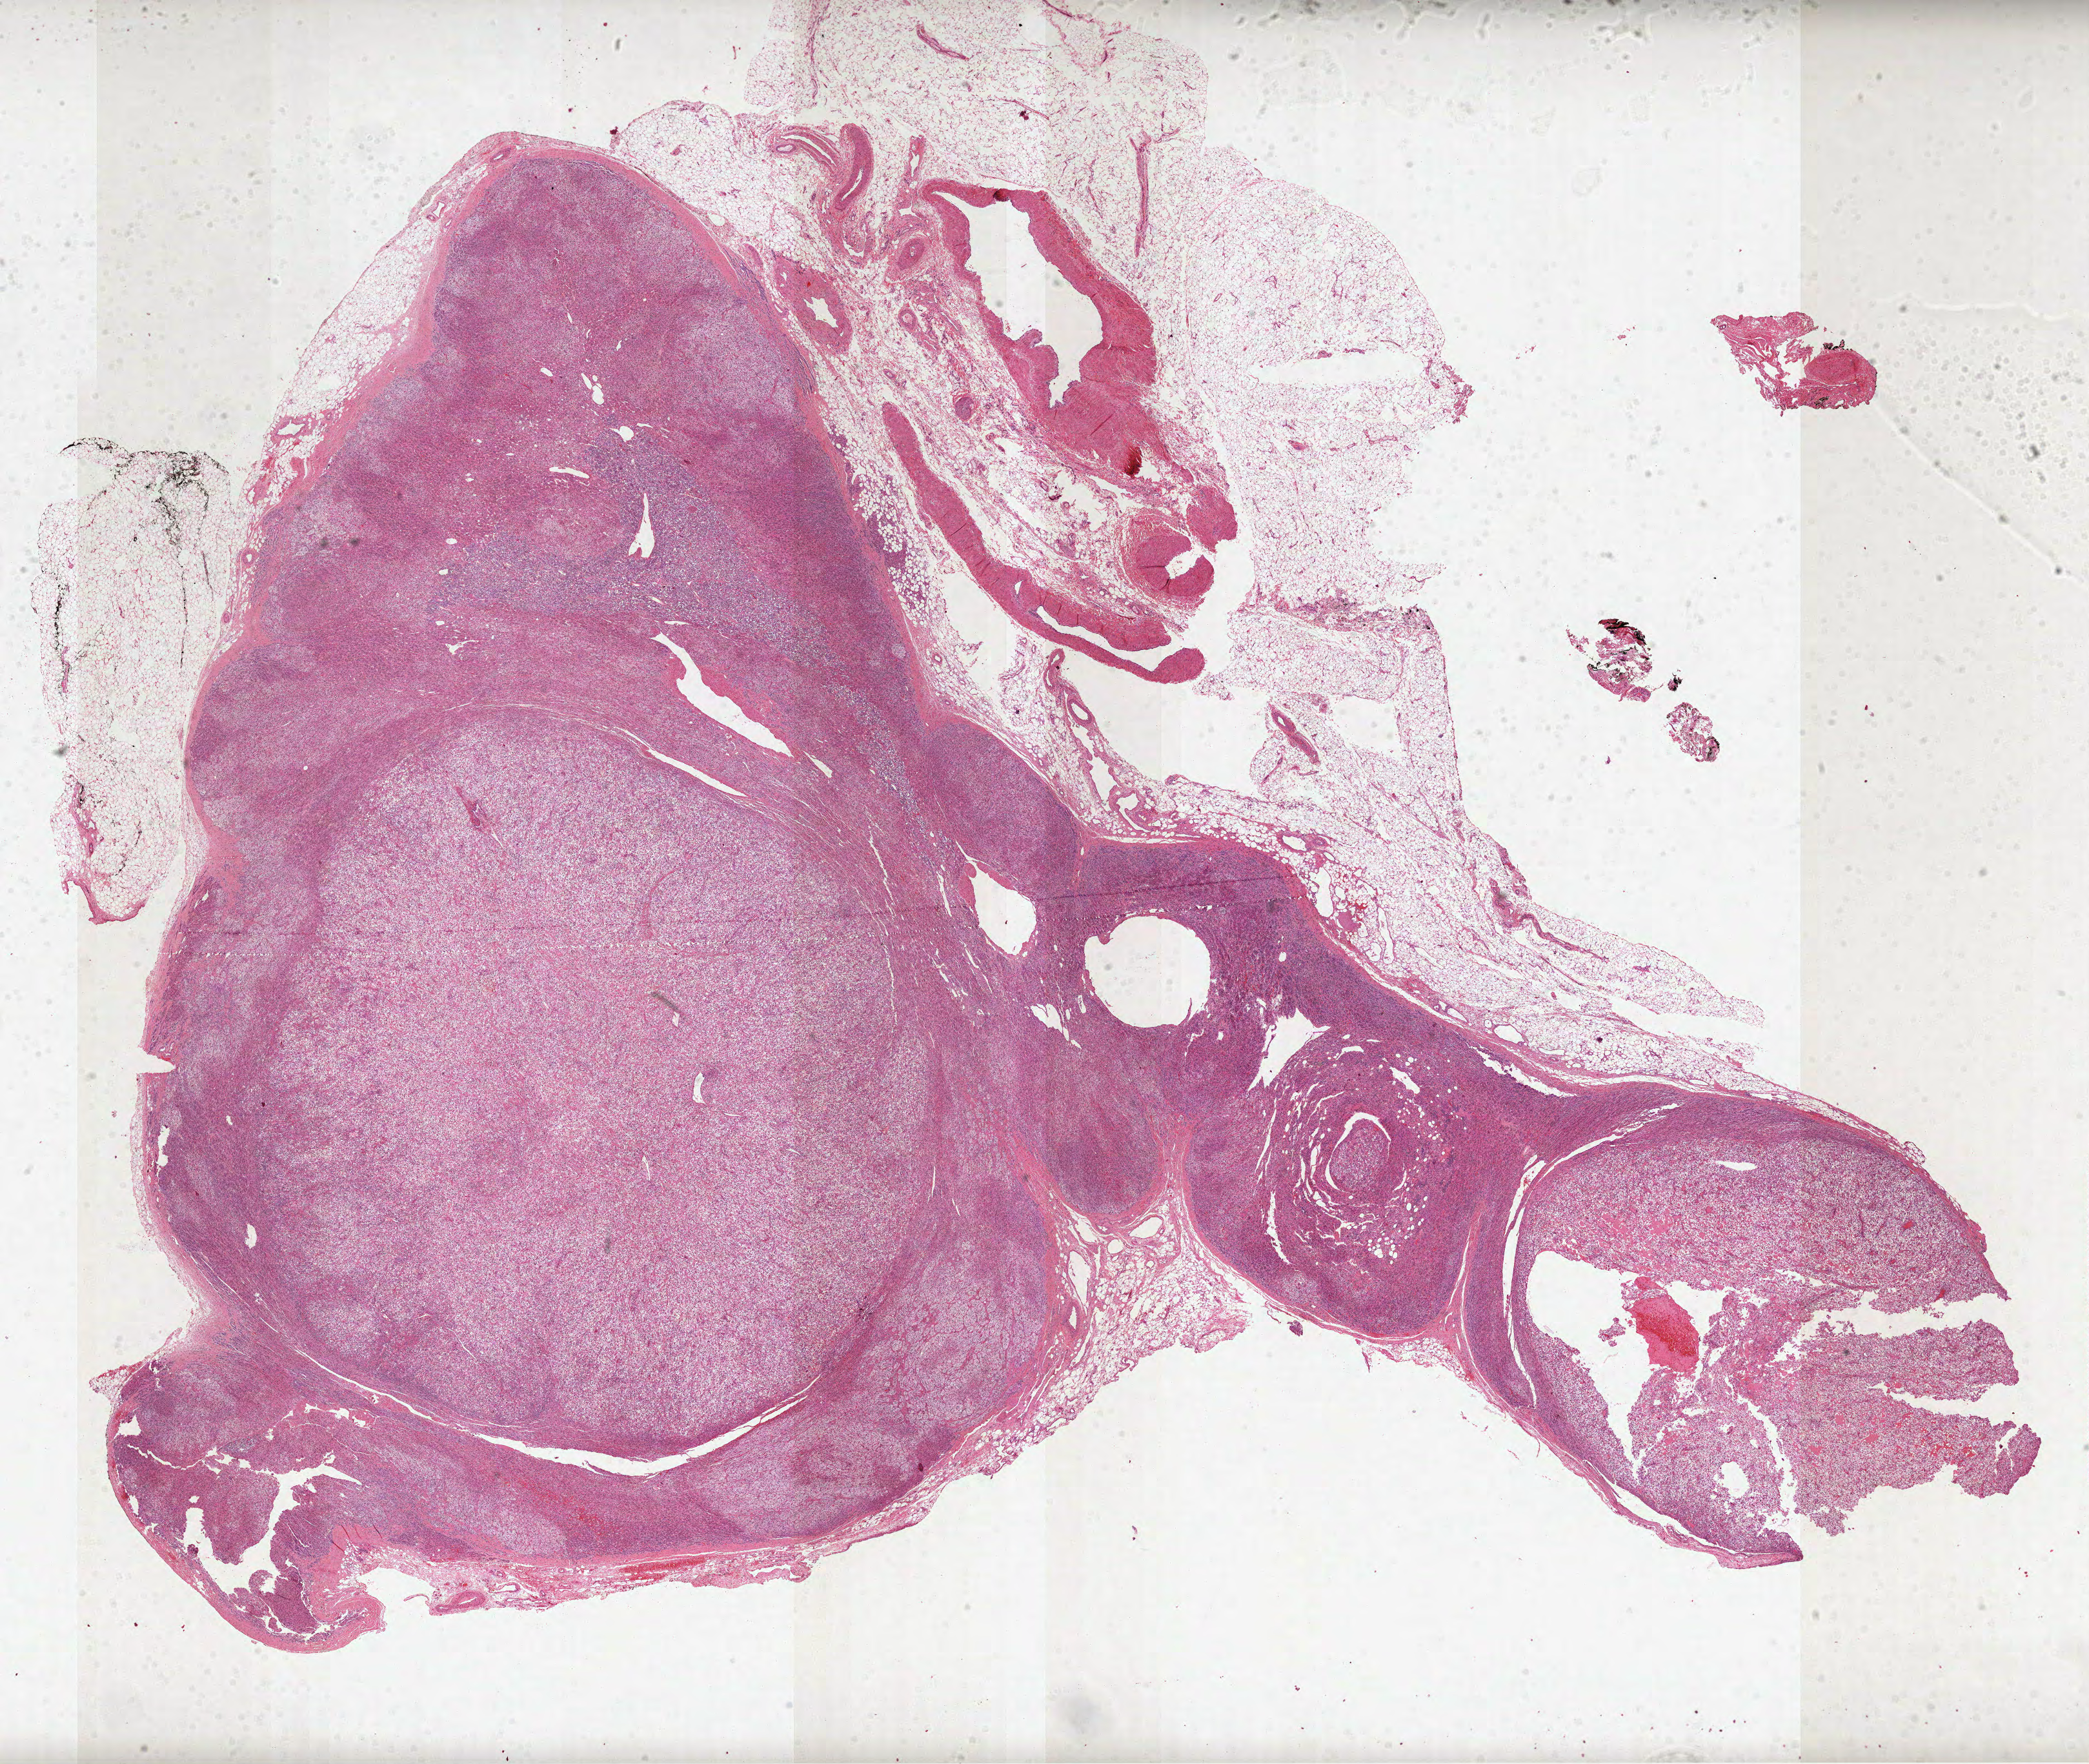
Whole-slide histology image, H&E-stained, shown as a low-resolution overview of the whole scanned area (about 26.1 x 22.0 mm), formalin-fixed paraffin-embedded (FFPE) diagnostic section, primary tumour sample from the kidney. Patient: male, age at initial diagnosis 65 years. Histologic grade: G3 (poorly differentiated).
Diagnosis: Clear cell adenocarcinoma, NOS. AJCC pathologic stage: IV. Lymph nodes positive (case pathology): 0 of 3 examined. TNM: T4 N0 M1.